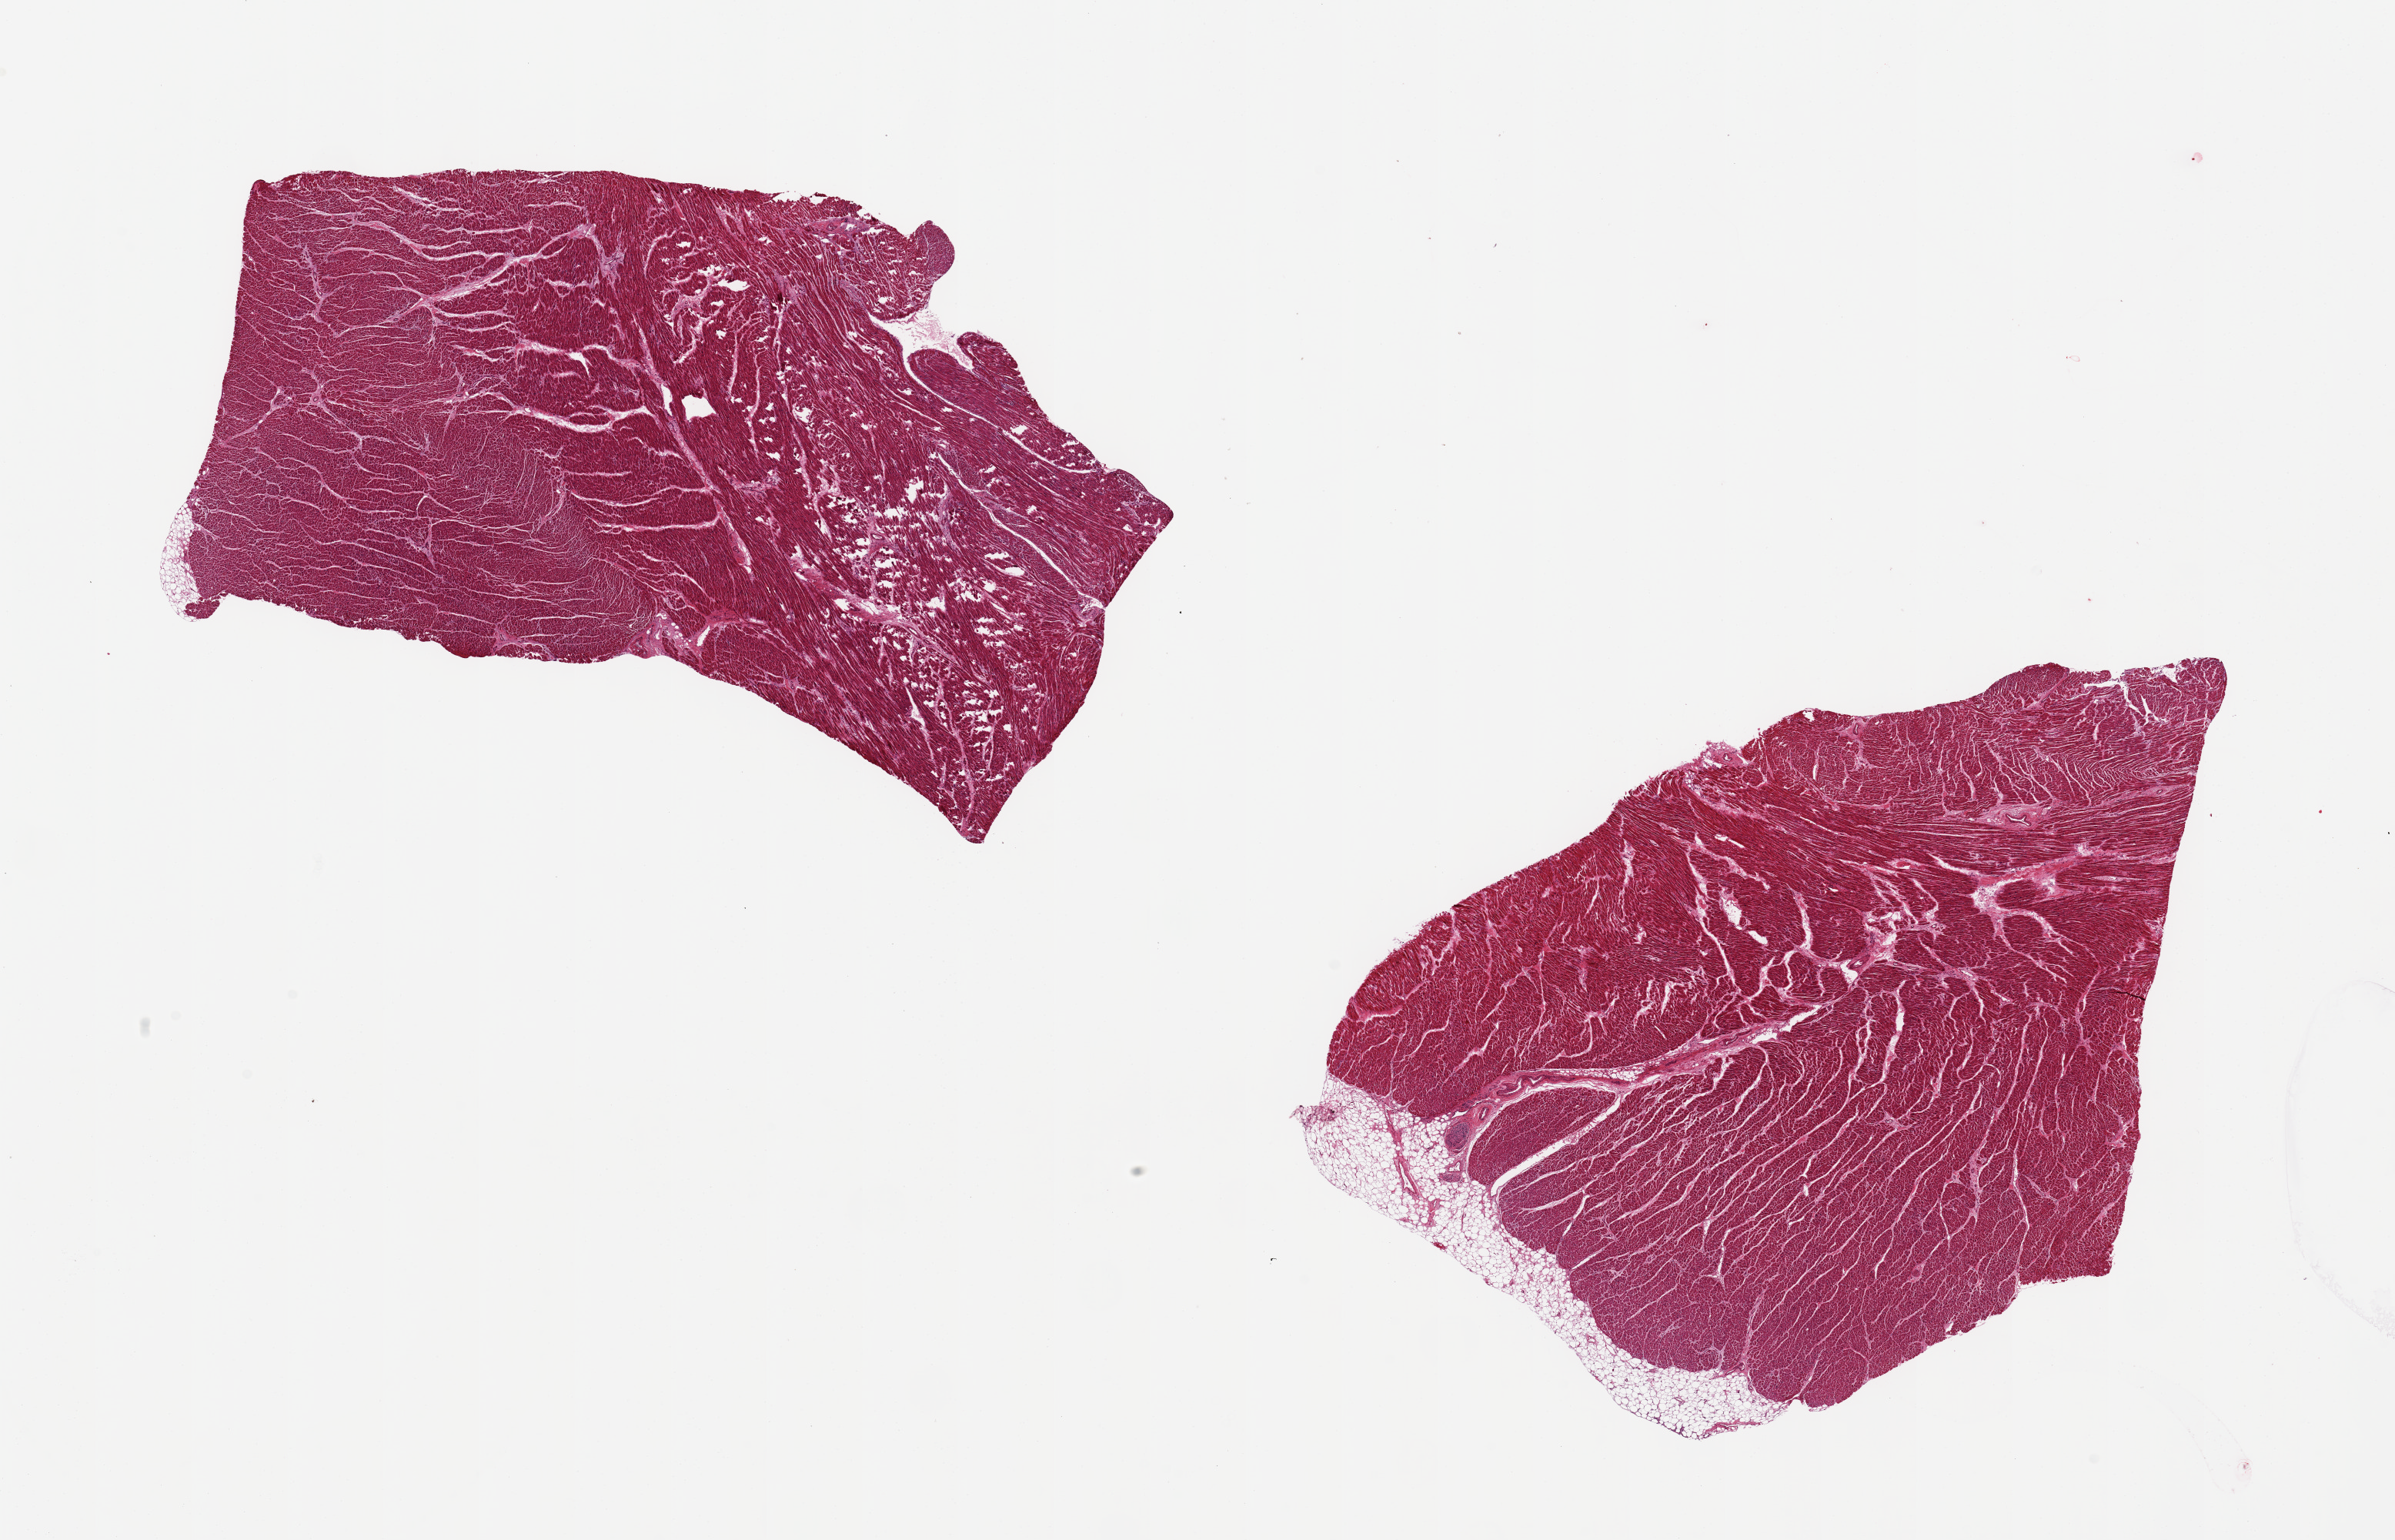
Whole-slide image, hematoxylin and eosin (H&E) stain, shown as a low-resolution overview of the whole scanned area (about 24.6 x 15.8 mm). PAXgene-fixed paraffin-embedded (PFPE) section. Sampled site (target tissue): heart. Donor tissue sample. Donor sex: female.
Pathologist's review note for this sample: 2 pieces ~10x5mm. one piece partially fixed (fractures).